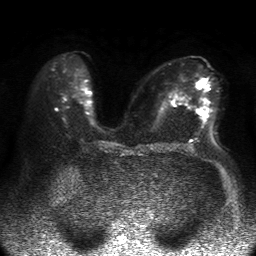
Breast MRI, one axial slice. Slice 22 of 50 in the series (ordered by position). Diffusion-weighted series; image 2 of 4 stored at this slice position (different b-values; order by instance number). 1.5 T. 4 mm slice thickness. 256 × 256 image matrix, field of view 360 × 360 mm. Female patient.
Annotated regions visible in this slice (outlined manually by an expert reader):
- tumour on diffusion-weighted imaging: bounding box (x1, y1, x2, y2) in pixels: (197, 80, 207, 115)